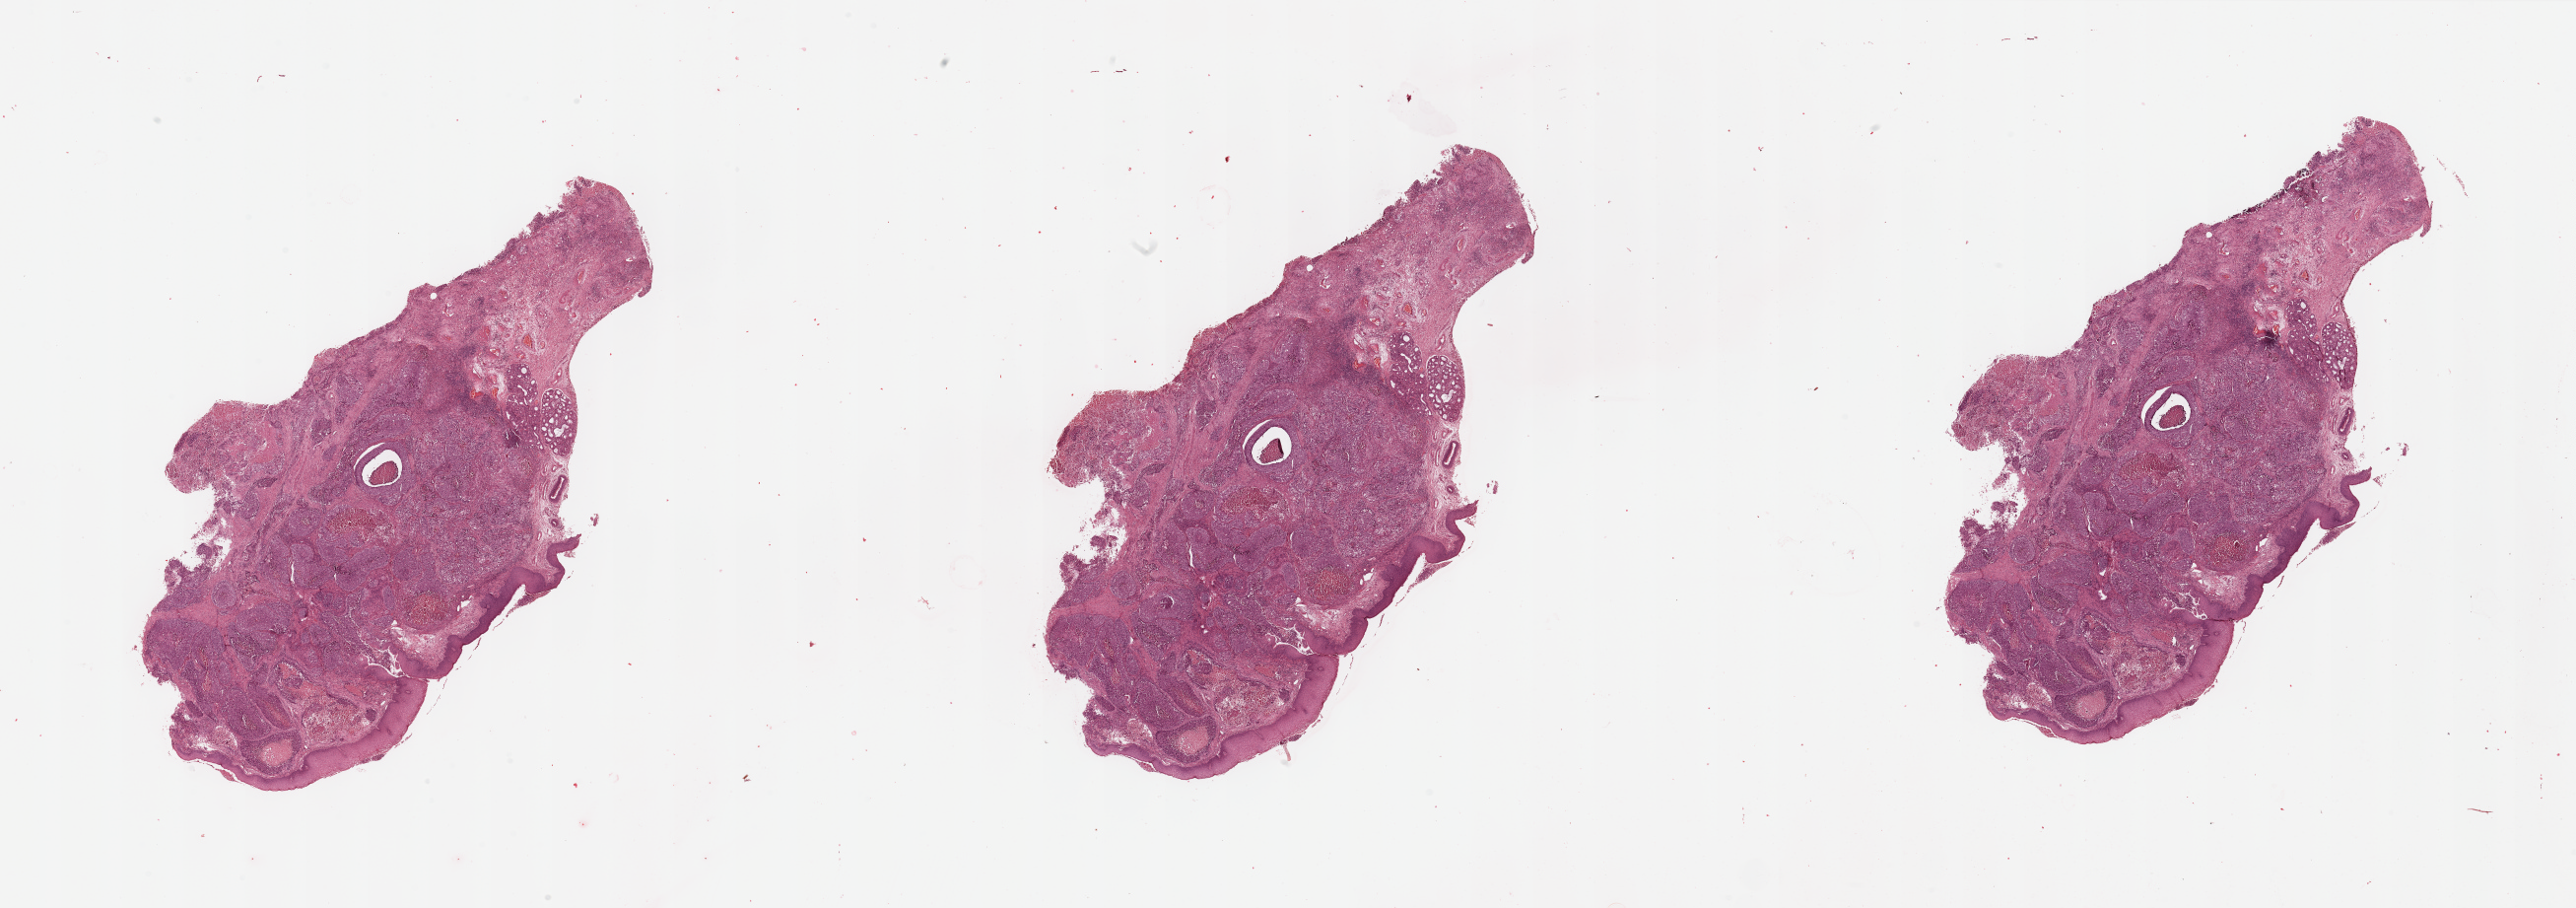
Hematoxylin and eosin (H&E) stained whole-slide image — shown as a low-resolution overview of the whole scanned area (about 41.3 x 14.6 mm, slide scanned at 20x); tumour tissue sample, sampled site: larynx. Patient: male, age 64 years. Histologic grade: G3 (poorly differentiated). Pathologist review of this section (percent, as recorded): tumour nuclei 60%, necrosis 10%.
* AJCC pathologic stage: II
* primary tumour site (as recorded): larynx
* histologic diagnosis: Squamous cell carcinoma, NOS